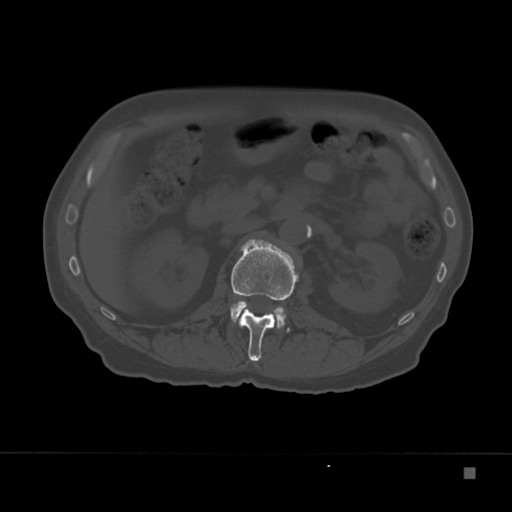
CT including the spine, one axial slice. Slice 105 of 332 in the series (ordered by position). Reconstruction kernel Br40s. 120 kVp. Bone window (W 1800 / L 400 HU). 1.5 mm slice thickness. 512 × 512 image matrix, field of view 389 × 389 mm. Patient: male, 72 years. Case-level facts recorded for this patient, not image findings: primary cancer: skeletal.
Structures marked on this image (semi-automatic segmentation, software-assisted and operator-edited):
- L1 vertebra: box from (x=231, y=239) to (x=299, y=362) px
- L2 vertebra: (x=230, y=302)–(x=290, y=332)